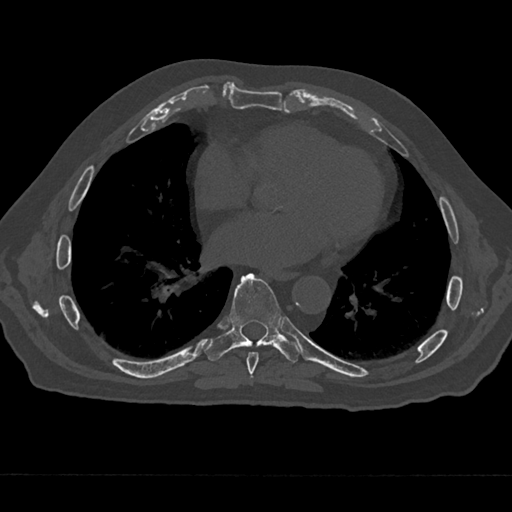
CT including the spine, one axial slice; slice 334 of 797 in the series (ordered by position); bone window (W 1800 / L 400 HU); 0.5 mm slice thickness; 512 × 512 image matrix, field of view 377 × 377 mm. Male patient, age 75 years. Case-level facts recorded for this patient, not image findings: primary cancer: renal.
Annotated regions visible in this slice (semi-automatic segmentation, software-assisted and operator-edited):
- T7 vertebra: bounding box [x1, y1, x2, y2] px = [245, 352, 259, 378]
- T8 vertebra: [205, 273, 300, 362]